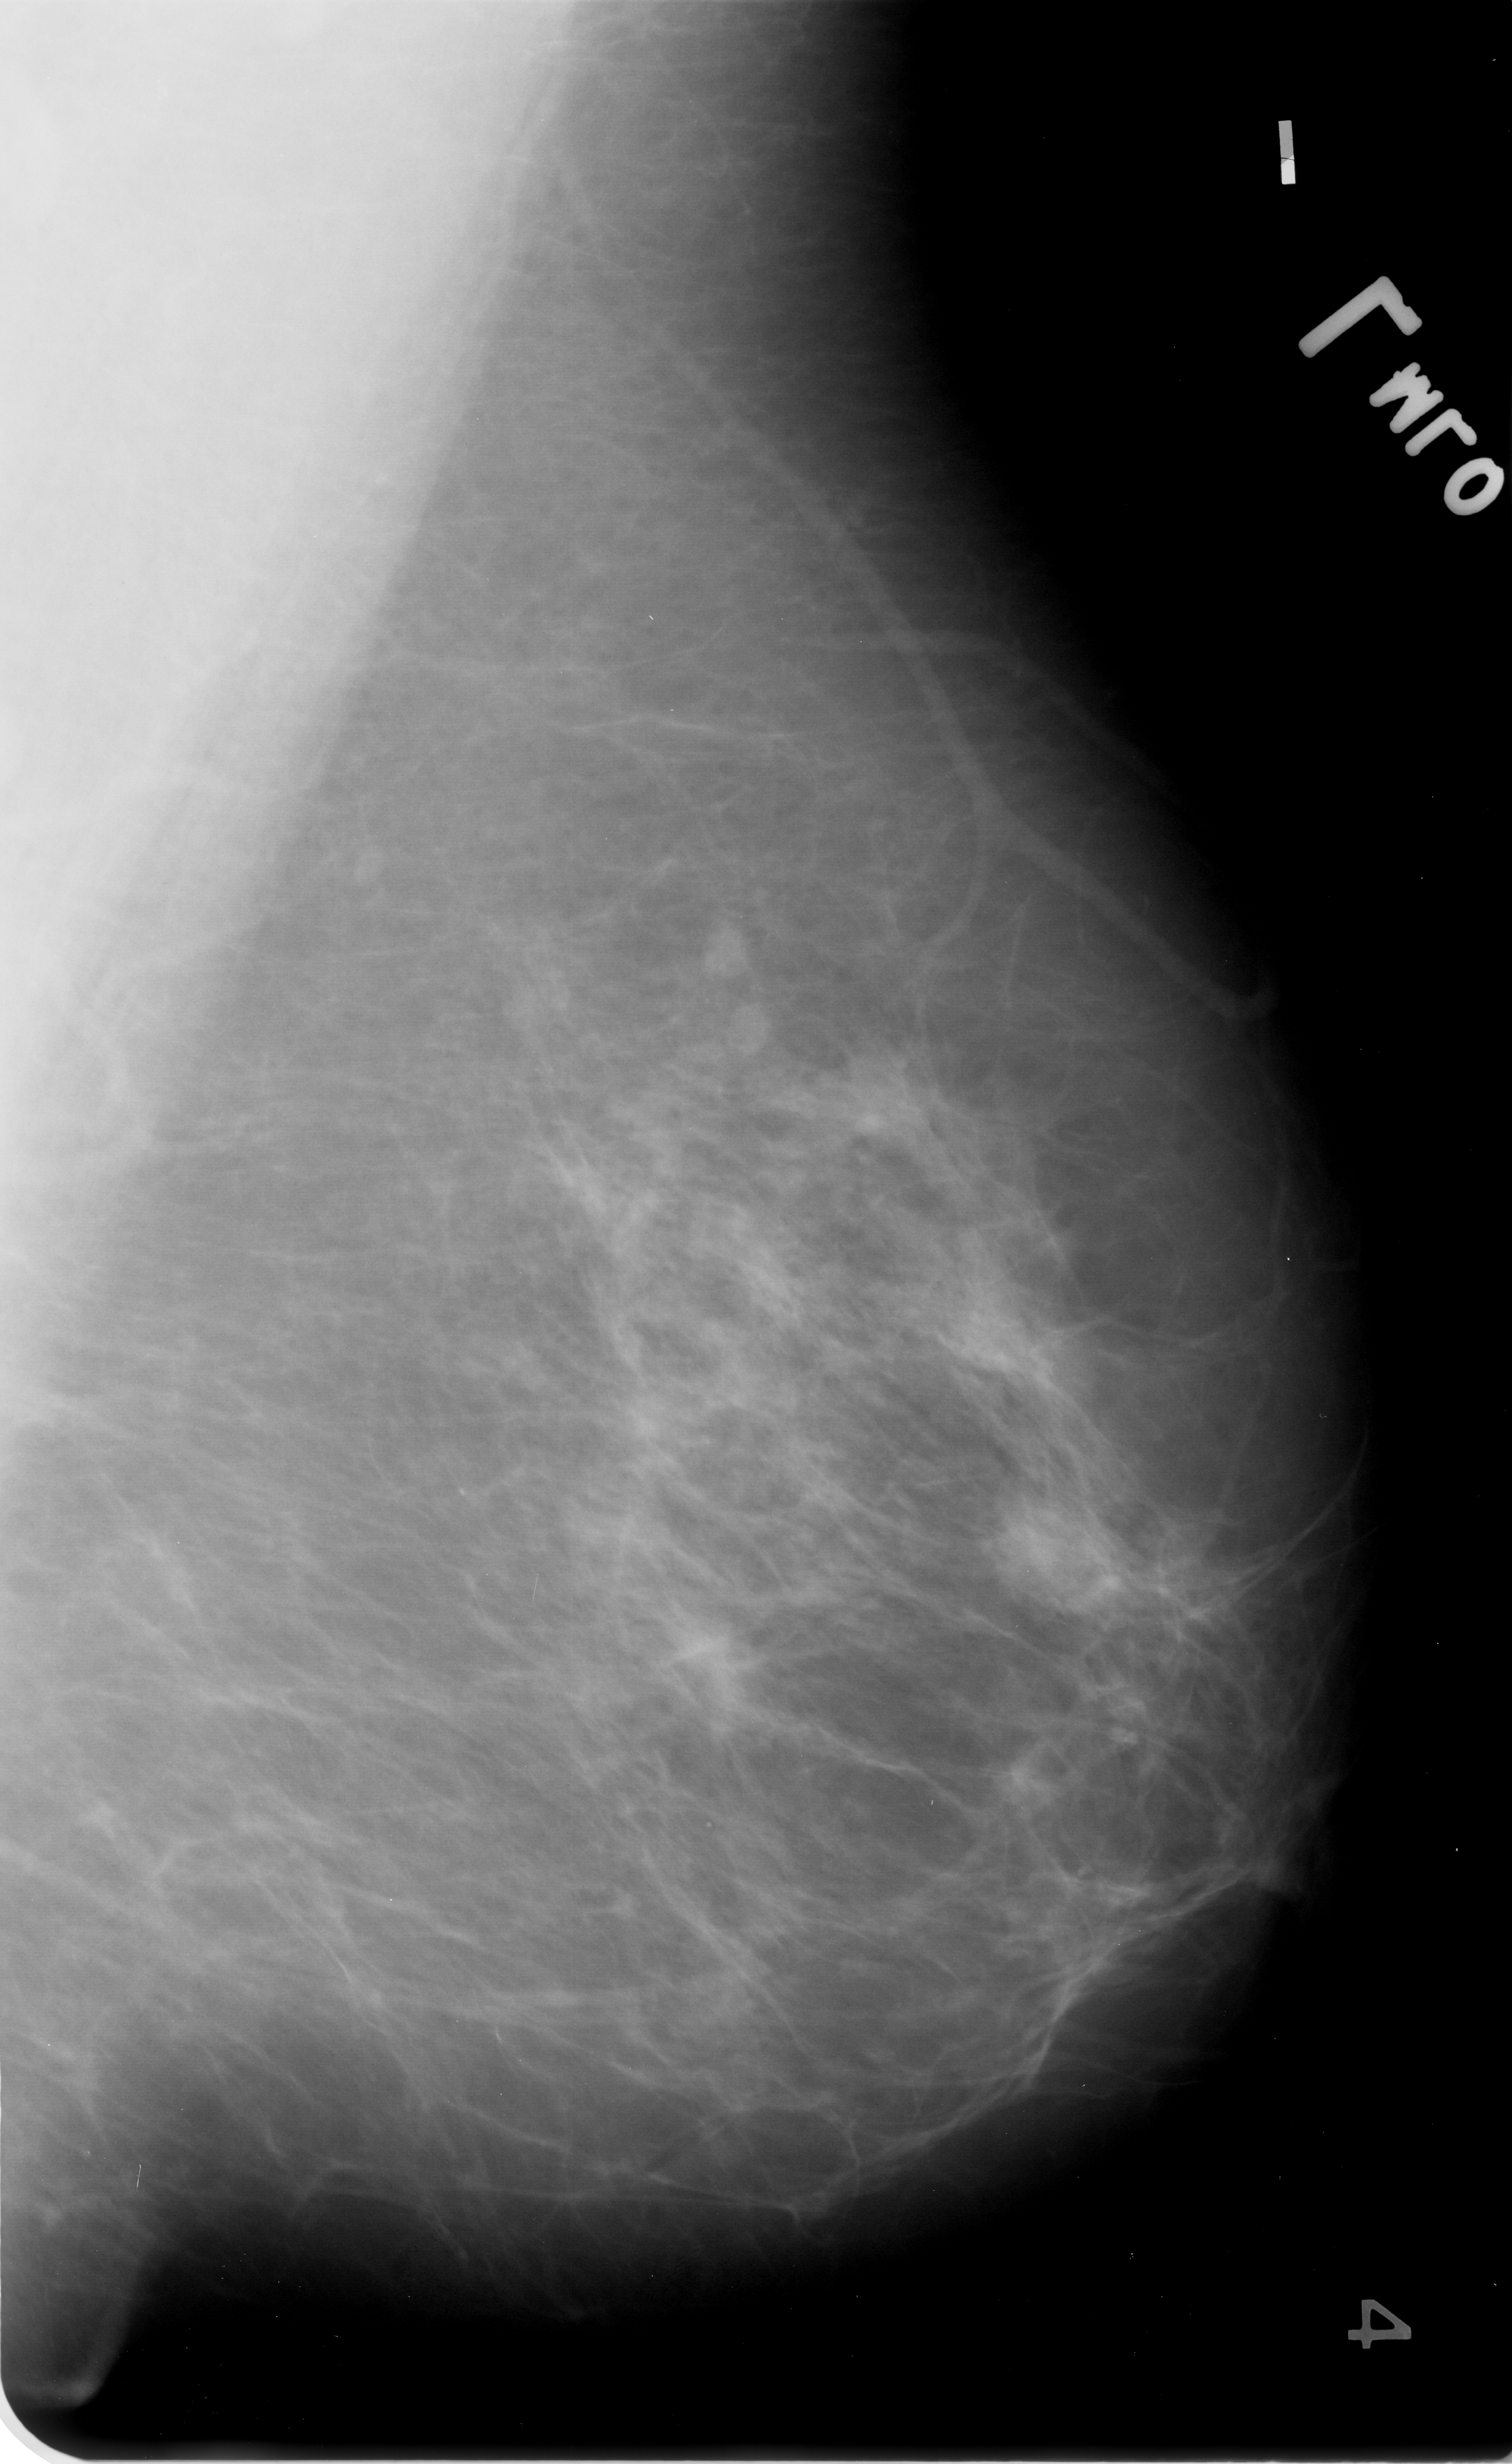
Scanned film-screen mammogram; left breast; MLO view; BI-RADS breast density category 2 (scale 1–4).
- Finding: mass, shape oval, margins obscured / ill defined; BI-RADS assessment category 3; pathology (as recorded): malignant.